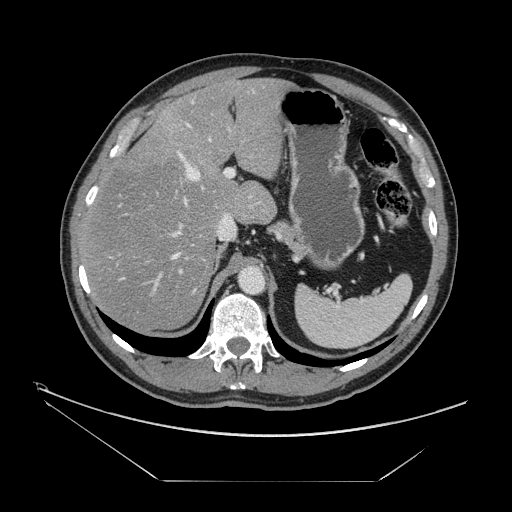
Contrast-enhanced abdominal CT, one axial slice; position 100 of 161 along the scan axis; reconstruction kernel STANDARD; 120 kVp; soft-tissue window (W 400 / L 40 HU); 512 × 512 image matrix, field of view 440 × 440 mm. Male patient, age 65 years. Case-level facts recorded for this patient, not image findings: diagnosis: colorectal cancer liver metastases, imaged before liver resection; multiple liver metastases: yes; largest metastasis: 4.2 cm; disease in both lobes: yes.
Structures marked on this image (manually delineated by an expert):
- hepatic veins: bounding box <120,124,211,280> (left, top, right, bottom; pixels)
- liver: <82,80,286,329>
- planned liver remnant (the part of the liver to remain after resection): <82,79,286,330>
- portal vein (with intrahepatic branches): <111,91,255,297>